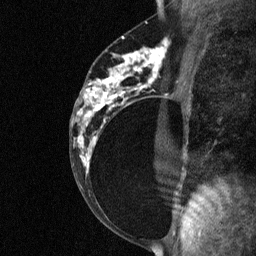
Breast MRI (dynamic contrast-enhanced), one sagittal slice. Slice 37 of 64 in the series (ordered by position). Dynamic contrast-enhanced study with each time point stored as its own series, time point 2 of 3 at this slice position (early post-contrast, ordered by acquisition time). 1.5 T. TE 4.8 ms, TR 27 ms. 2 mm slice thickness. 256 × 256 image matrix, field of view 180 × 180 mm. Female patient, age 34 years. Case-level facts recorded for this patient, not image findings: setting: breast cancer imaged before/during neoadjuvant chemotherapy; receptor status: HR-positive, HER2-negative.
Outlined on this slice (semi-automatically segmented with operator editing):
- analysis volume of interest (the breast-tissue region the enhancement analysis was run in; not a lesion): box from (x=78, y=44) to (x=181, y=191) px
- tumour enhancement mask (voxels above the 90 % enhancement threshold inside the analysis volume of interest): (x=80, y=44)–(x=168, y=167)